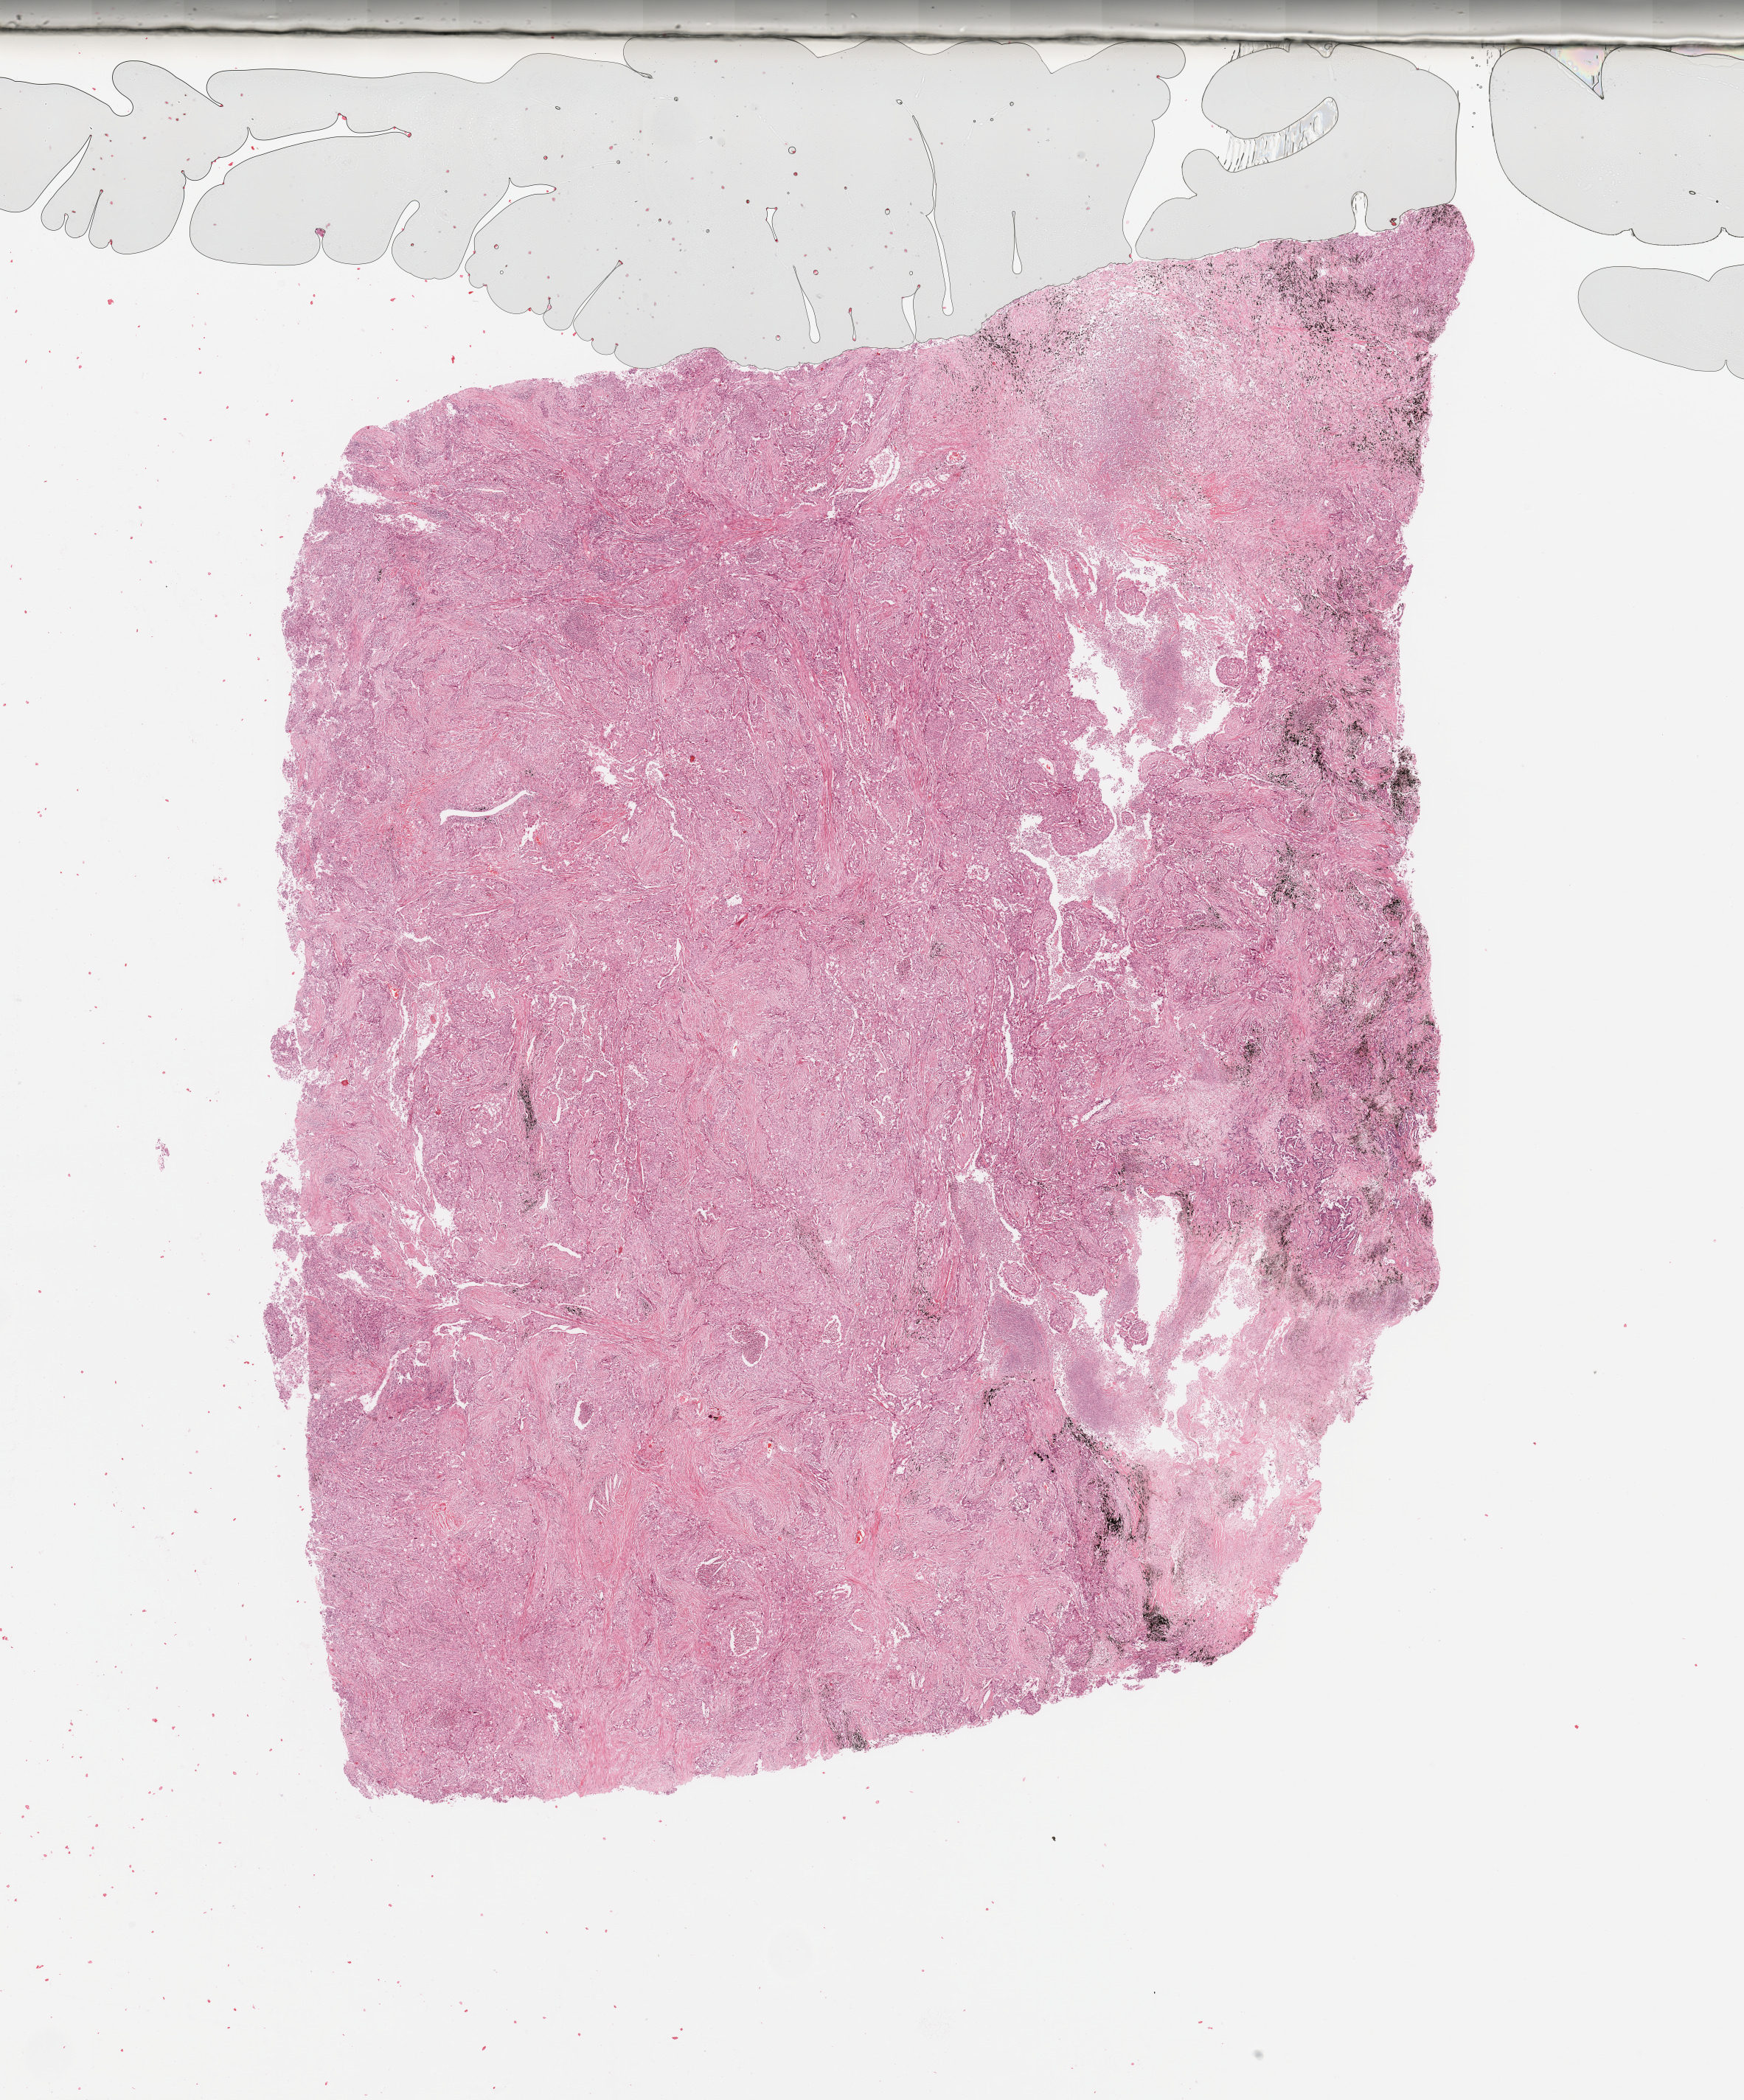
Whole-slide histology image, H&E — shown as a low-resolution overview of the whole scanned area (about 18.7 x 22.5 mm). Lung, tumour tissue. 58-year-old male patient. Histologic grade: G3 (poorly differentiated).
Histologic diagnosis: Adenocarcinoma, NOS. AJCC pathologic stage: IIA.